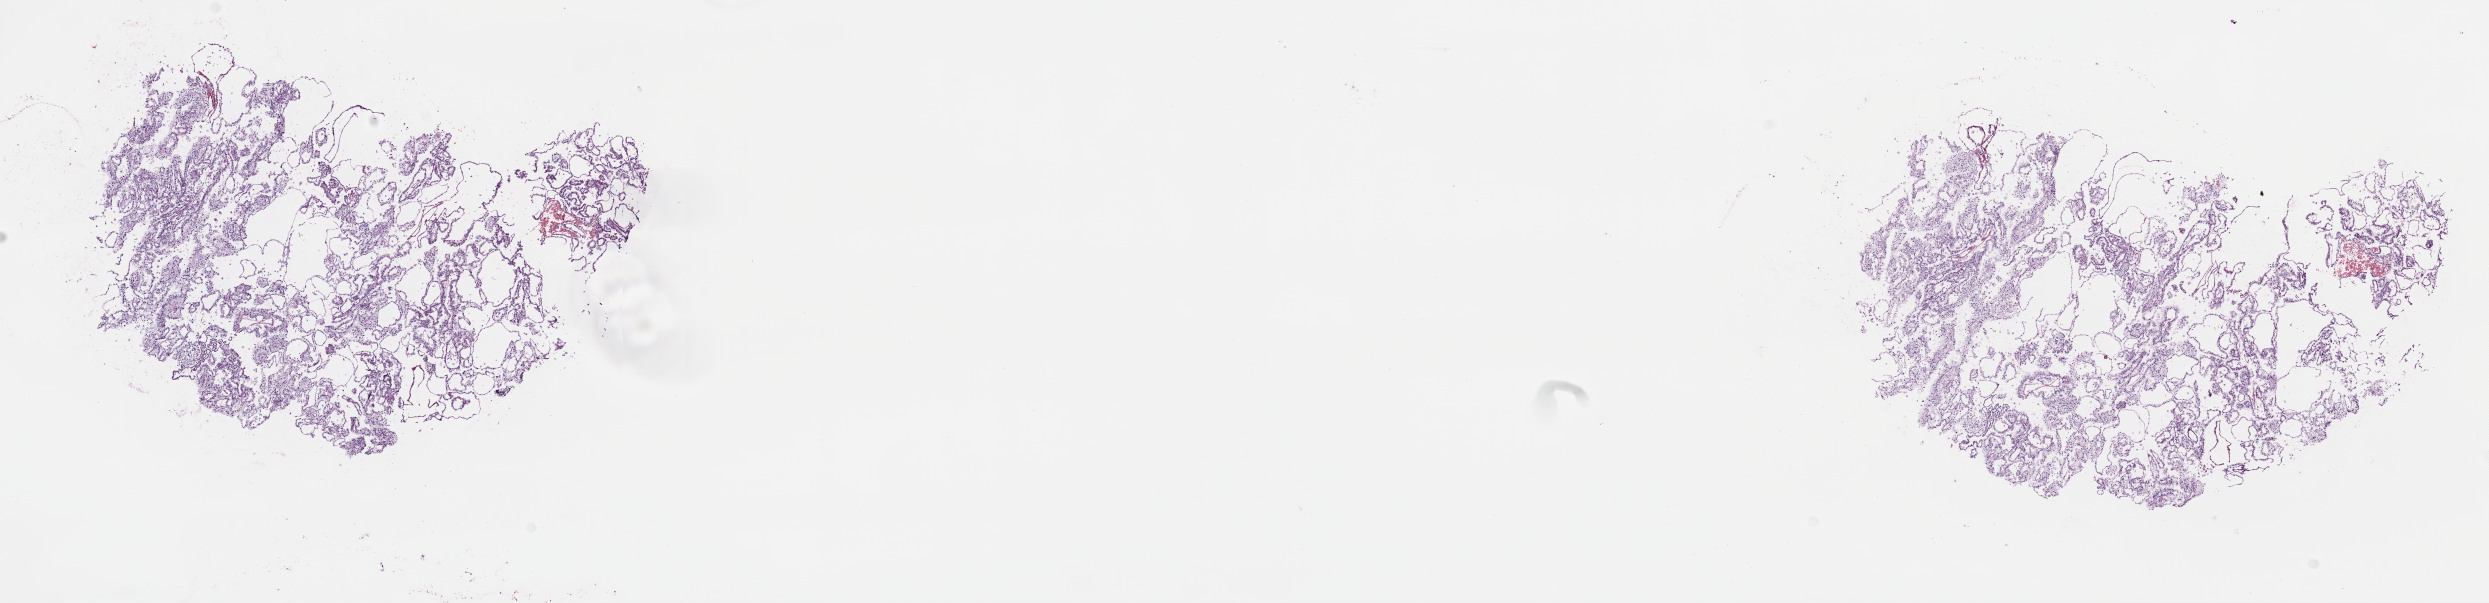
H&E whole-slide image — whole scanned area (about 20.1 x 4.9 mm) shown as a low-resolution overview, frozen section, primary tumour sample from the kidney. Female patient; age at initial diagnosis 66 years. Composition of this section per pathologist review: tumour cells 85%, tumour nuclei 85%, normal cells 0%, stromal cells 15%, necrosis 0%. Infiltration values recorded for this section: lymphocyte infiltration 0%, monocyte infiltration 3%, neutrophil infiltration 0%.
• lymph nodes positive (case pathology): 0 of 16 examined
• AJCC pathologic stage: I (7th edition)
• histologic diagnosis: Papillary adenocarcinoma, NOS